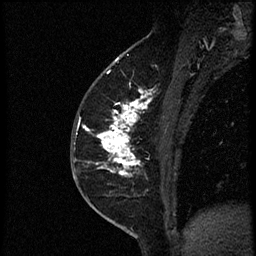
Breast MRI (dynamic contrast-enhanced), one sagittal slice; dynamic contrast-enhanced study with each time point stored as its own series, time point 2 of 4 at this slice position (early post-contrast, ordered by acquisition time); 1.5 T; TE 4.2 ms, TR 18.9 ms; 256 × 256 image matrix, field of view 200 × 200 mm. Female patient. Case-level facts recorded for this patient, not image findings: setting: breast cancer imaged before/during neoadjuvant chemotherapy; receptor status: HER2-positive.
Outlined on this slice (semi-automatically segmented with operator editing):
- analysis volume of interest (the breast-tissue region the enhancement analysis was run in; not a lesion): box from (x=80, y=87) to (x=174, y=189) px
- tumour enhancement mask (voxels above the 100 % enhancement threshold inside the analysis volume of interest): (x=84, y=90)–(x=154, y=177)